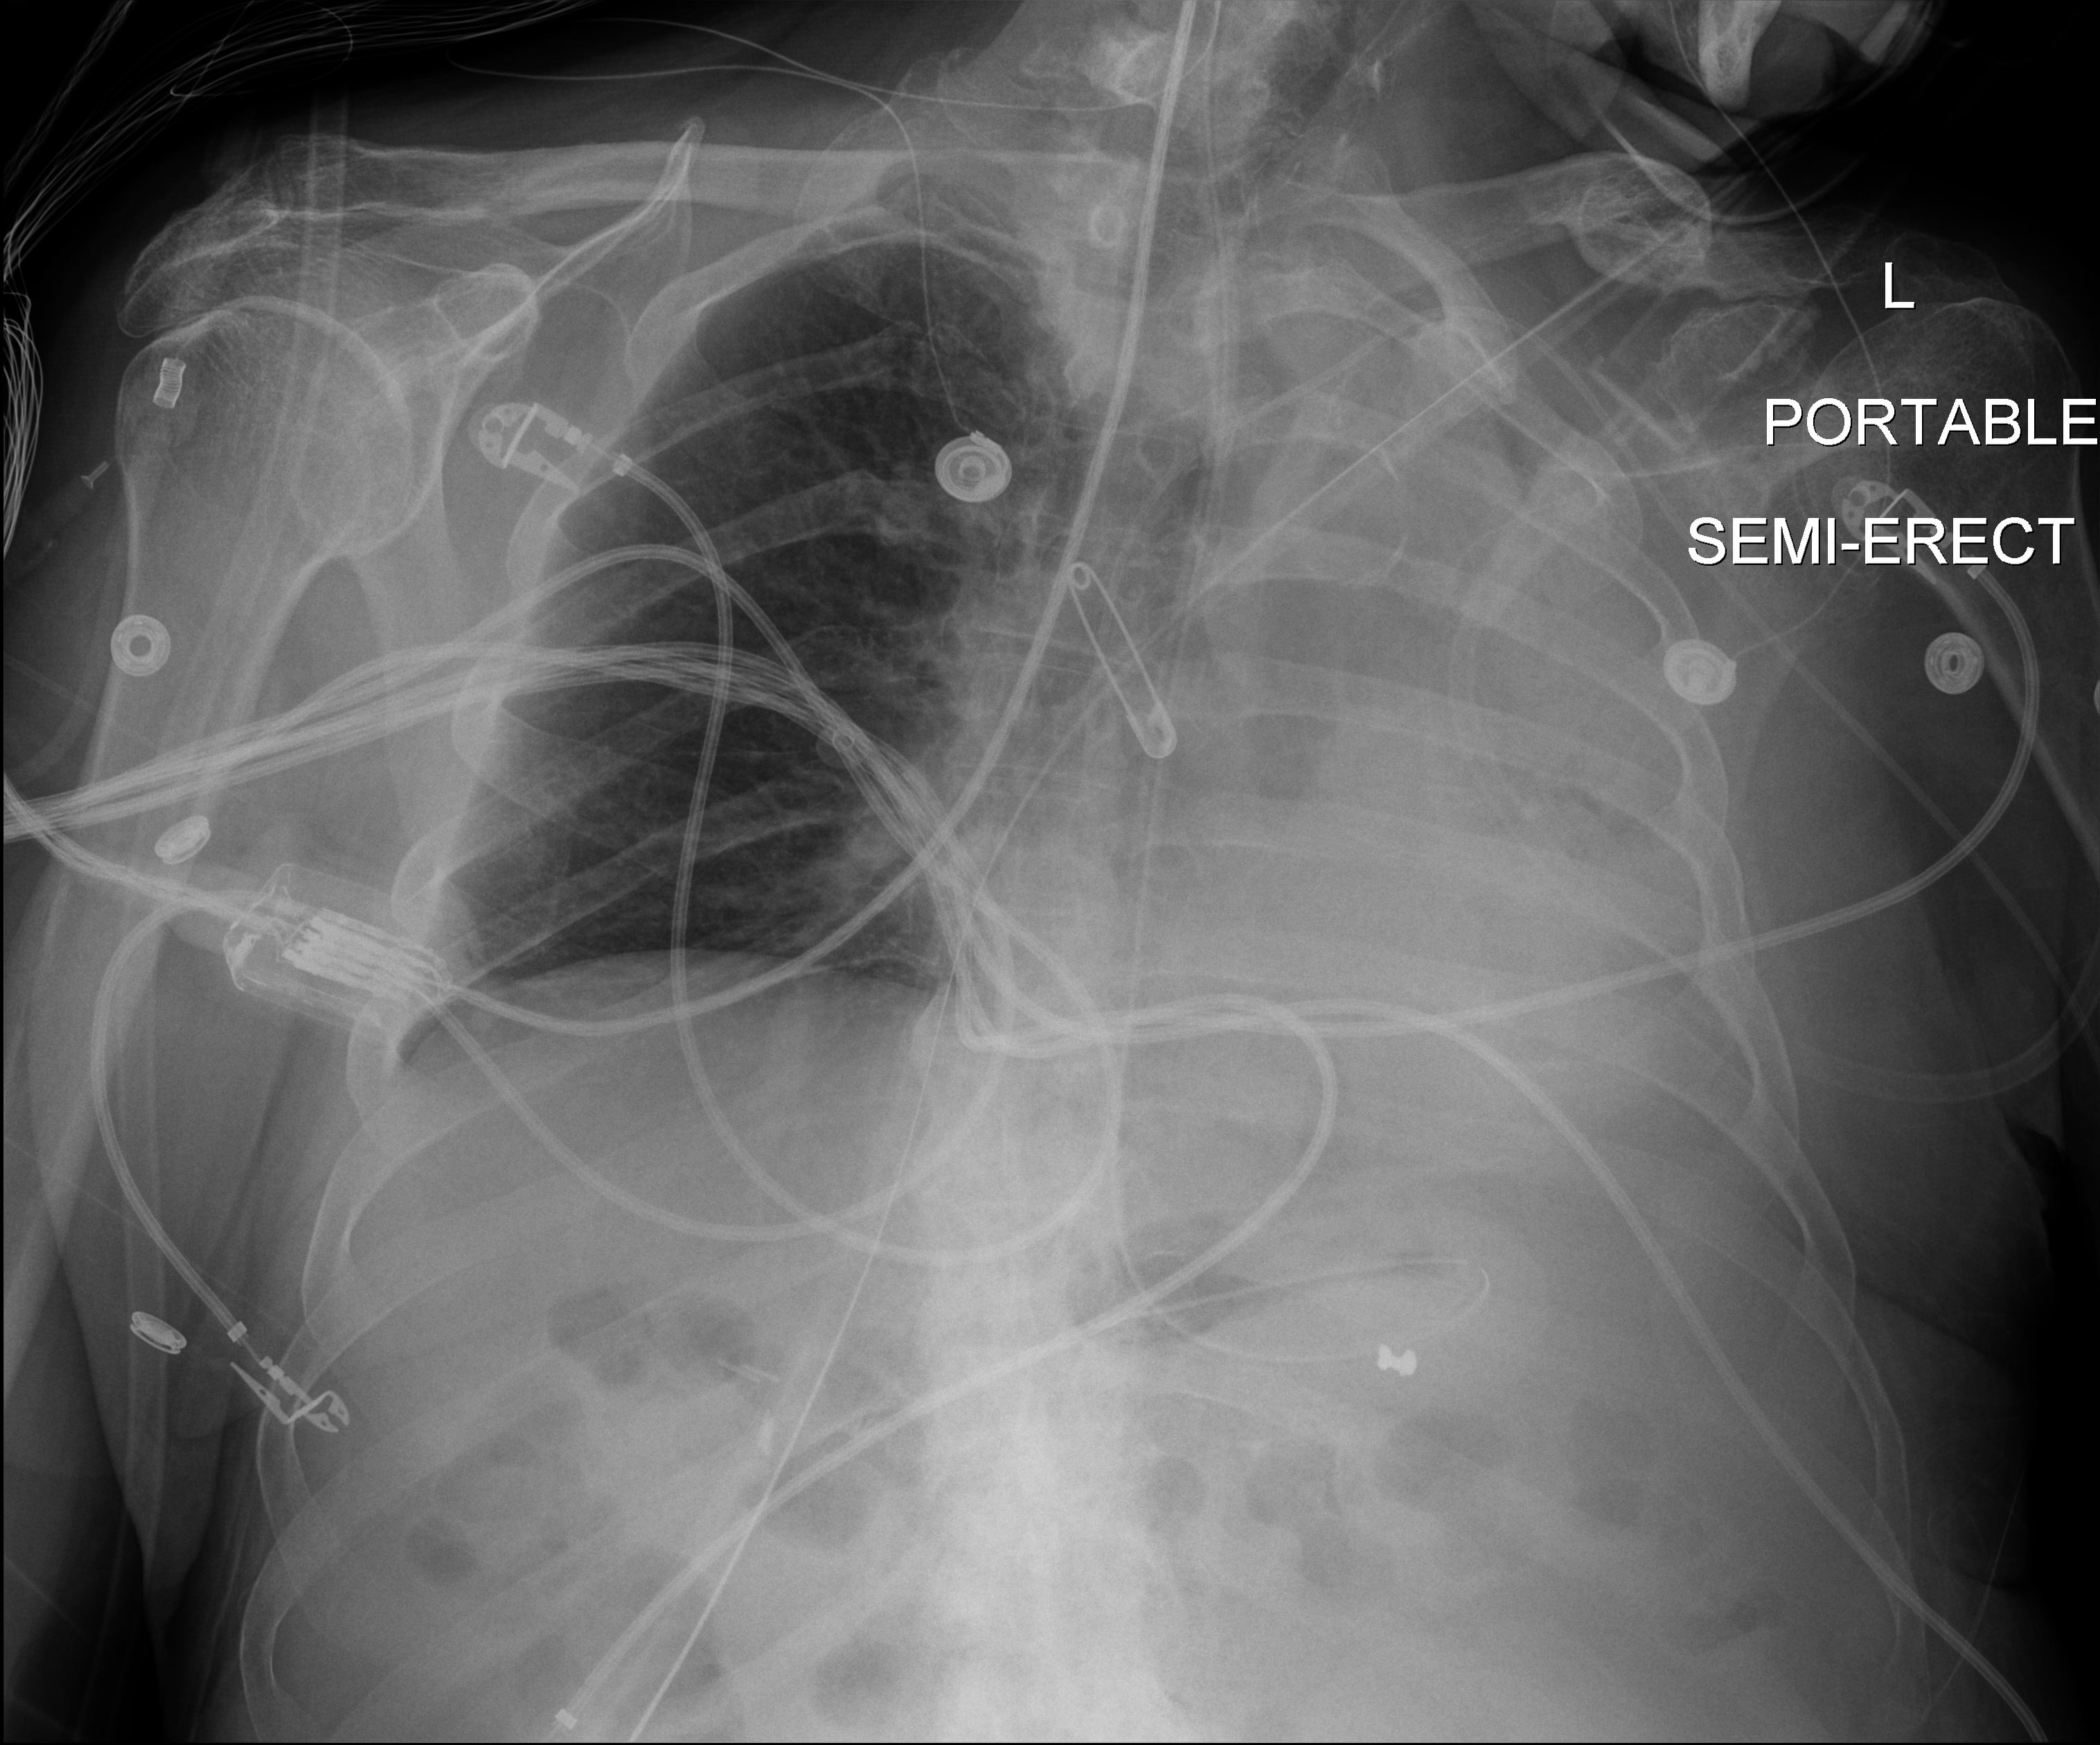
Portable chest radiograph; anteroposterior (AP) projection. Male patient hospitalised with COVID-19, age 60–74 years.
Hospital-stay facts (about this admission, not read from this image; timing relative to this image not recorded):
- length of hospital stay: 5 days
- mechanically ventilated during this hospital stay: no
- admitted to intensive care during this hospital stay: no